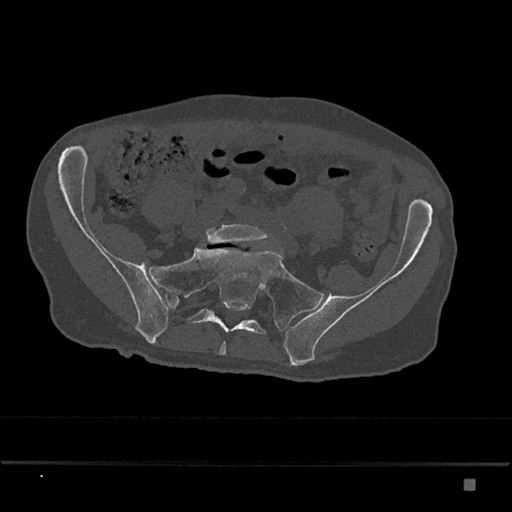
CT including the spine, one axial slice; position 217 of 797 along the scan axis; reconstruction kernel Br40s/3; 120 kVp; bone window (W 1800 / L 400 HU); 0.5 mm slice thickness; 512 × 512 image matrix, field of view 390 × 390 mm. Patient: male, 72 years. From the clinical record (not read from this slice): primary cancer: prostate.
Annotated regions visible in this slice (semi-automatically segmented with operator editing):
- L5 vertebra: bounding box <206,224,268,243> (left, top, right, bottom; pixels)